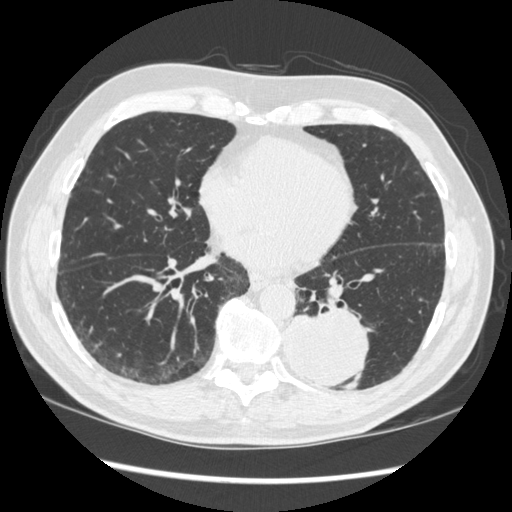
Chest CT (low-dose screening protocol), one axial image; baseline screening round; lung window (W 1500 / L -600 HU); 1.25 mm slice thickness; standard (soft-tissue) reconstruction kernel (STANDARD); 120 kVp. Male, age 72 years at enrolment.
• Expert-annotated lung lesion, bounding box (x1, y1, x2, y2) in pixels: (271, 298, 375, 387).
• The screening reader recorded 2 non-calcified nodules or masses ≥4 mm on this exam; which of them this box marks is not recorded.
• Official screen result: positive, change unspecified: nodule(s) >= 4 mm or enlarging nodule(s), mass(es), or other non-specific abnormalities suspicious for lung cancer.
• Lung cancer was diagnosed 37 days after this screen: squamous cell carcinoma, NOS, left lower lobe, stage IIIA (AJCC 6th edition), 60 mm at pathology.